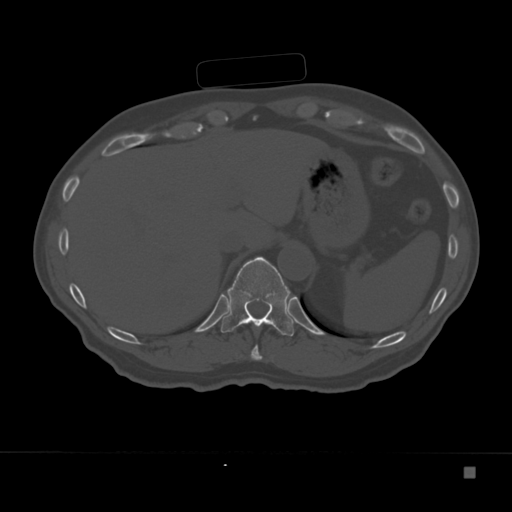
CT including the spine, one axial slice. Slice 157 of 332 in the series (ordered by position). Bone window (W 1800 / L 400 HU). 1.5 mm slice thickness. 512 × 512 image matrix, field of view 389 × 389 mm. Male patient, age 72 years. From the clinical record (not read from this slice): primary cancer: skeletal.
Annotated regions visible in this slice (semi-automatic segmentation, software-assisted and operator-edited):
- T10 vertebra: bounding box (x1, y1, x2, y2) in pixels: (251, 345, 262, 360)
- T11 vertebra: (220, 257, 295, 337)